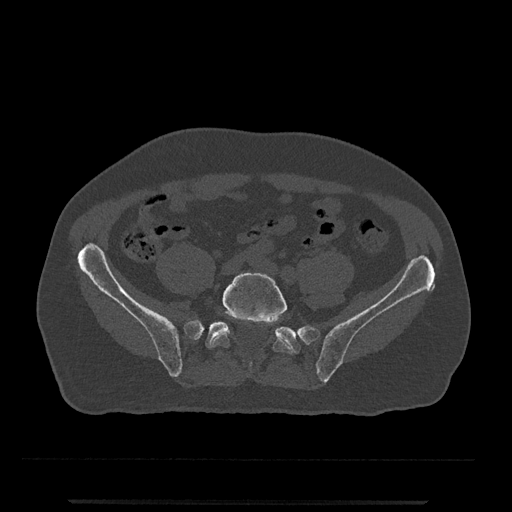
CT including the spine, one axial slice; position 50 of 797 along the scan axis; 120 kVp; bone window (W 1800 / L 400 HU); 0.5 mm slice thickness; 512 × 512 image matrix, field of view 419 × 419 mm. Male patient, age 63 years. Case-level facts recorded for this patient, not image findings: primary cancer: prostate.
Annotated regions visible in this slice (semi-automatically segmented with operator editing):
- L5 vertebra: bounding box <209,272,292,369> (left, top, right, bottom; pixels)